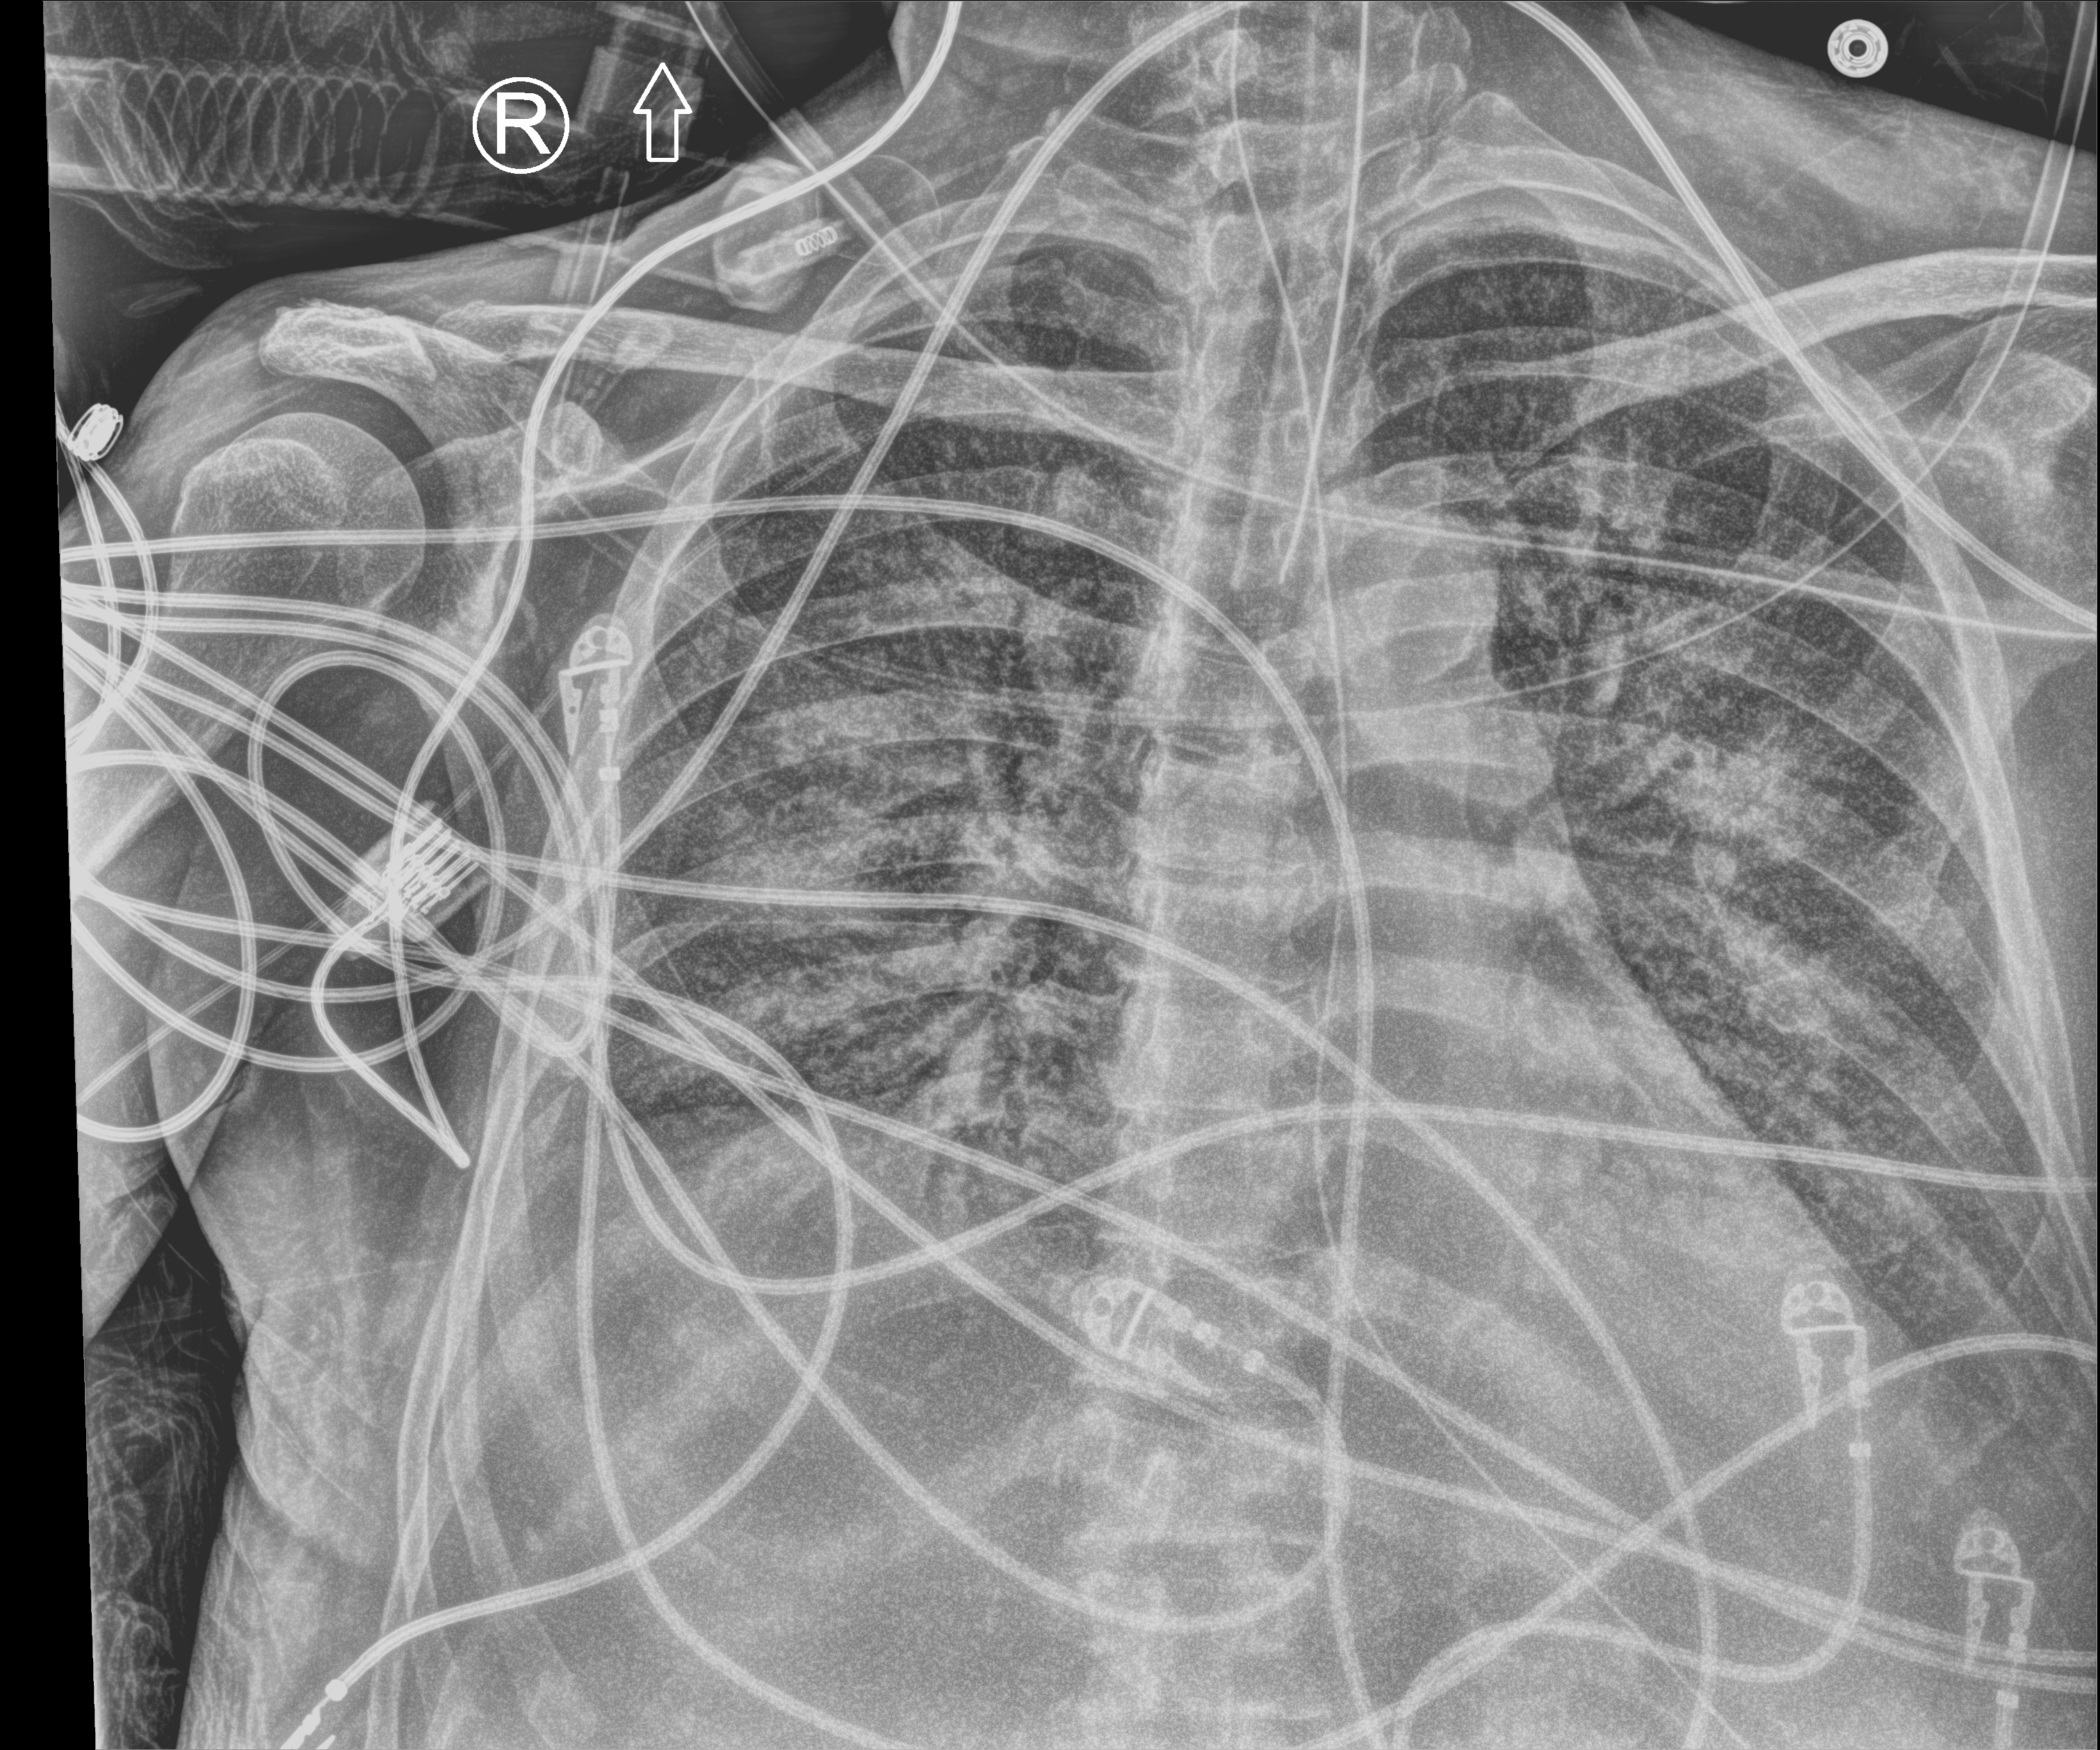
Chest X-ray (portable); anteroposterior (AP) projection. Patient hospitalised with COVID-19; male, aged 60–74 years.
From the hospital-stay record, not from the radiograph (when in the stay this image was taken is not recorded): admitted to intensive care during this hospital stay: yes.